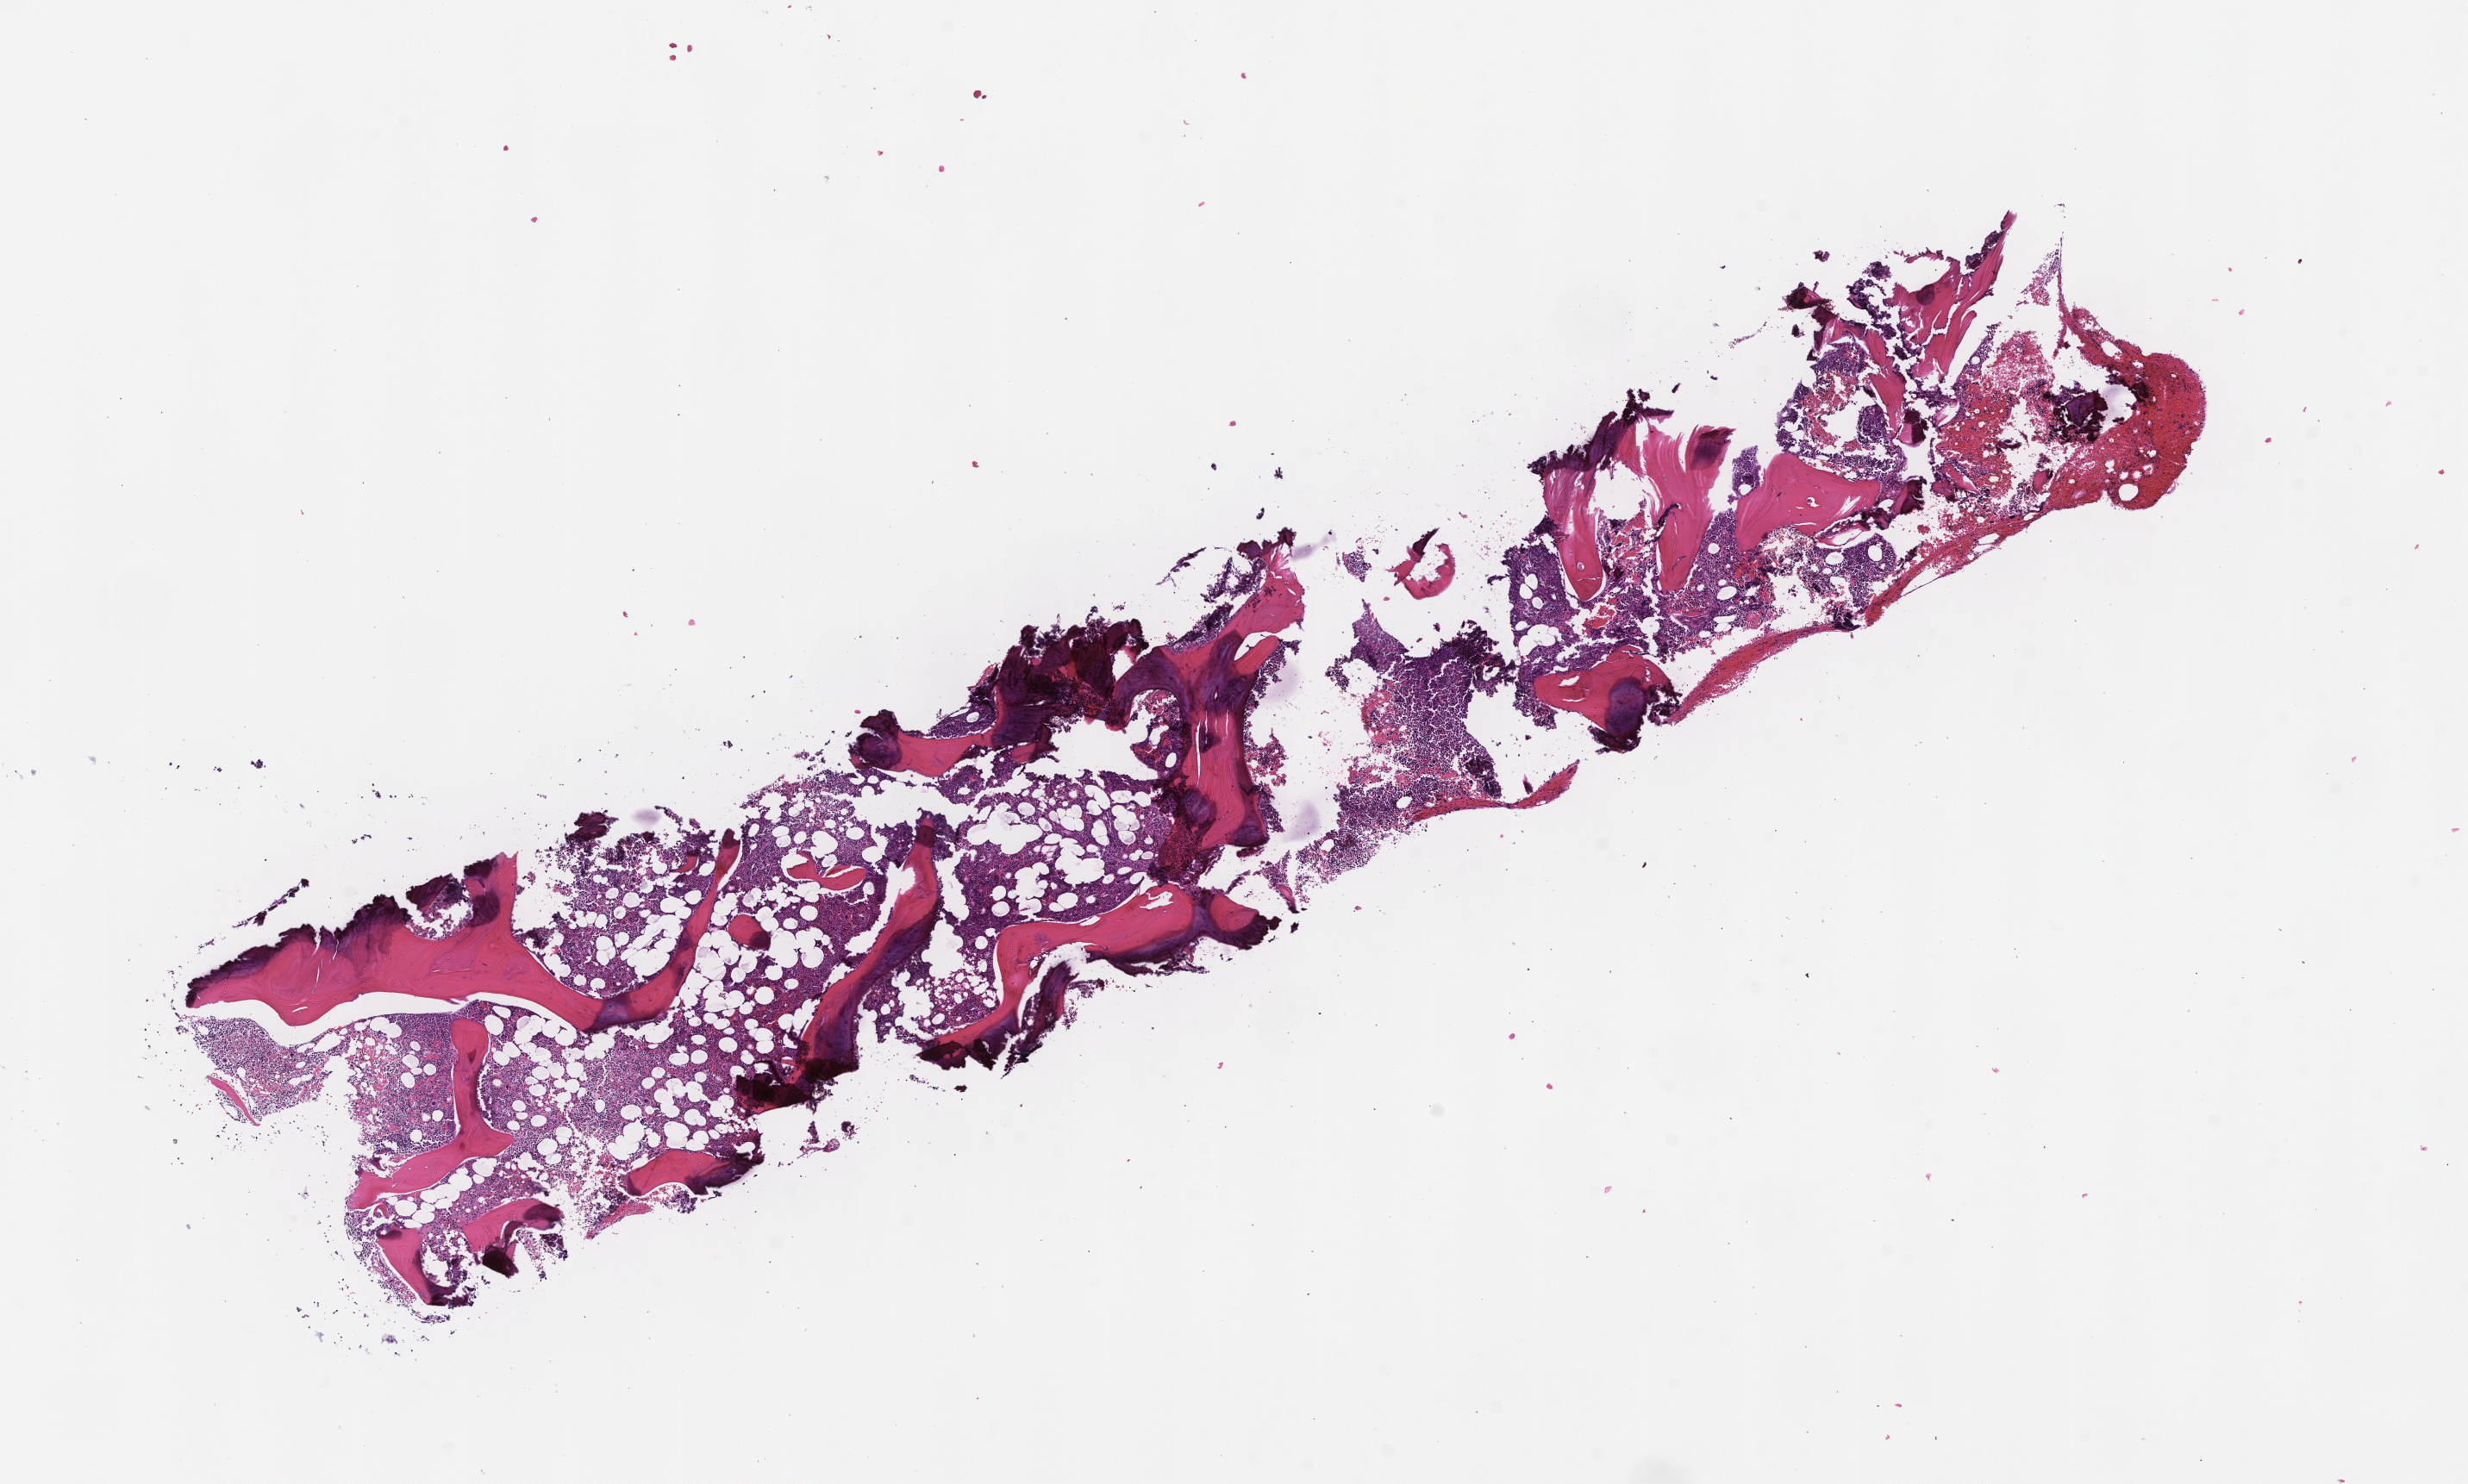
Hematoxylin and eosin (H&E) whole-slide image — shown as a low-resolution overview of the whole scanned area (about 11.6 x 7.0 mm), FFPE section, tissue site: bone marrow. Female patient.
Patient diagnosis: Plasma Cell Myeloma.